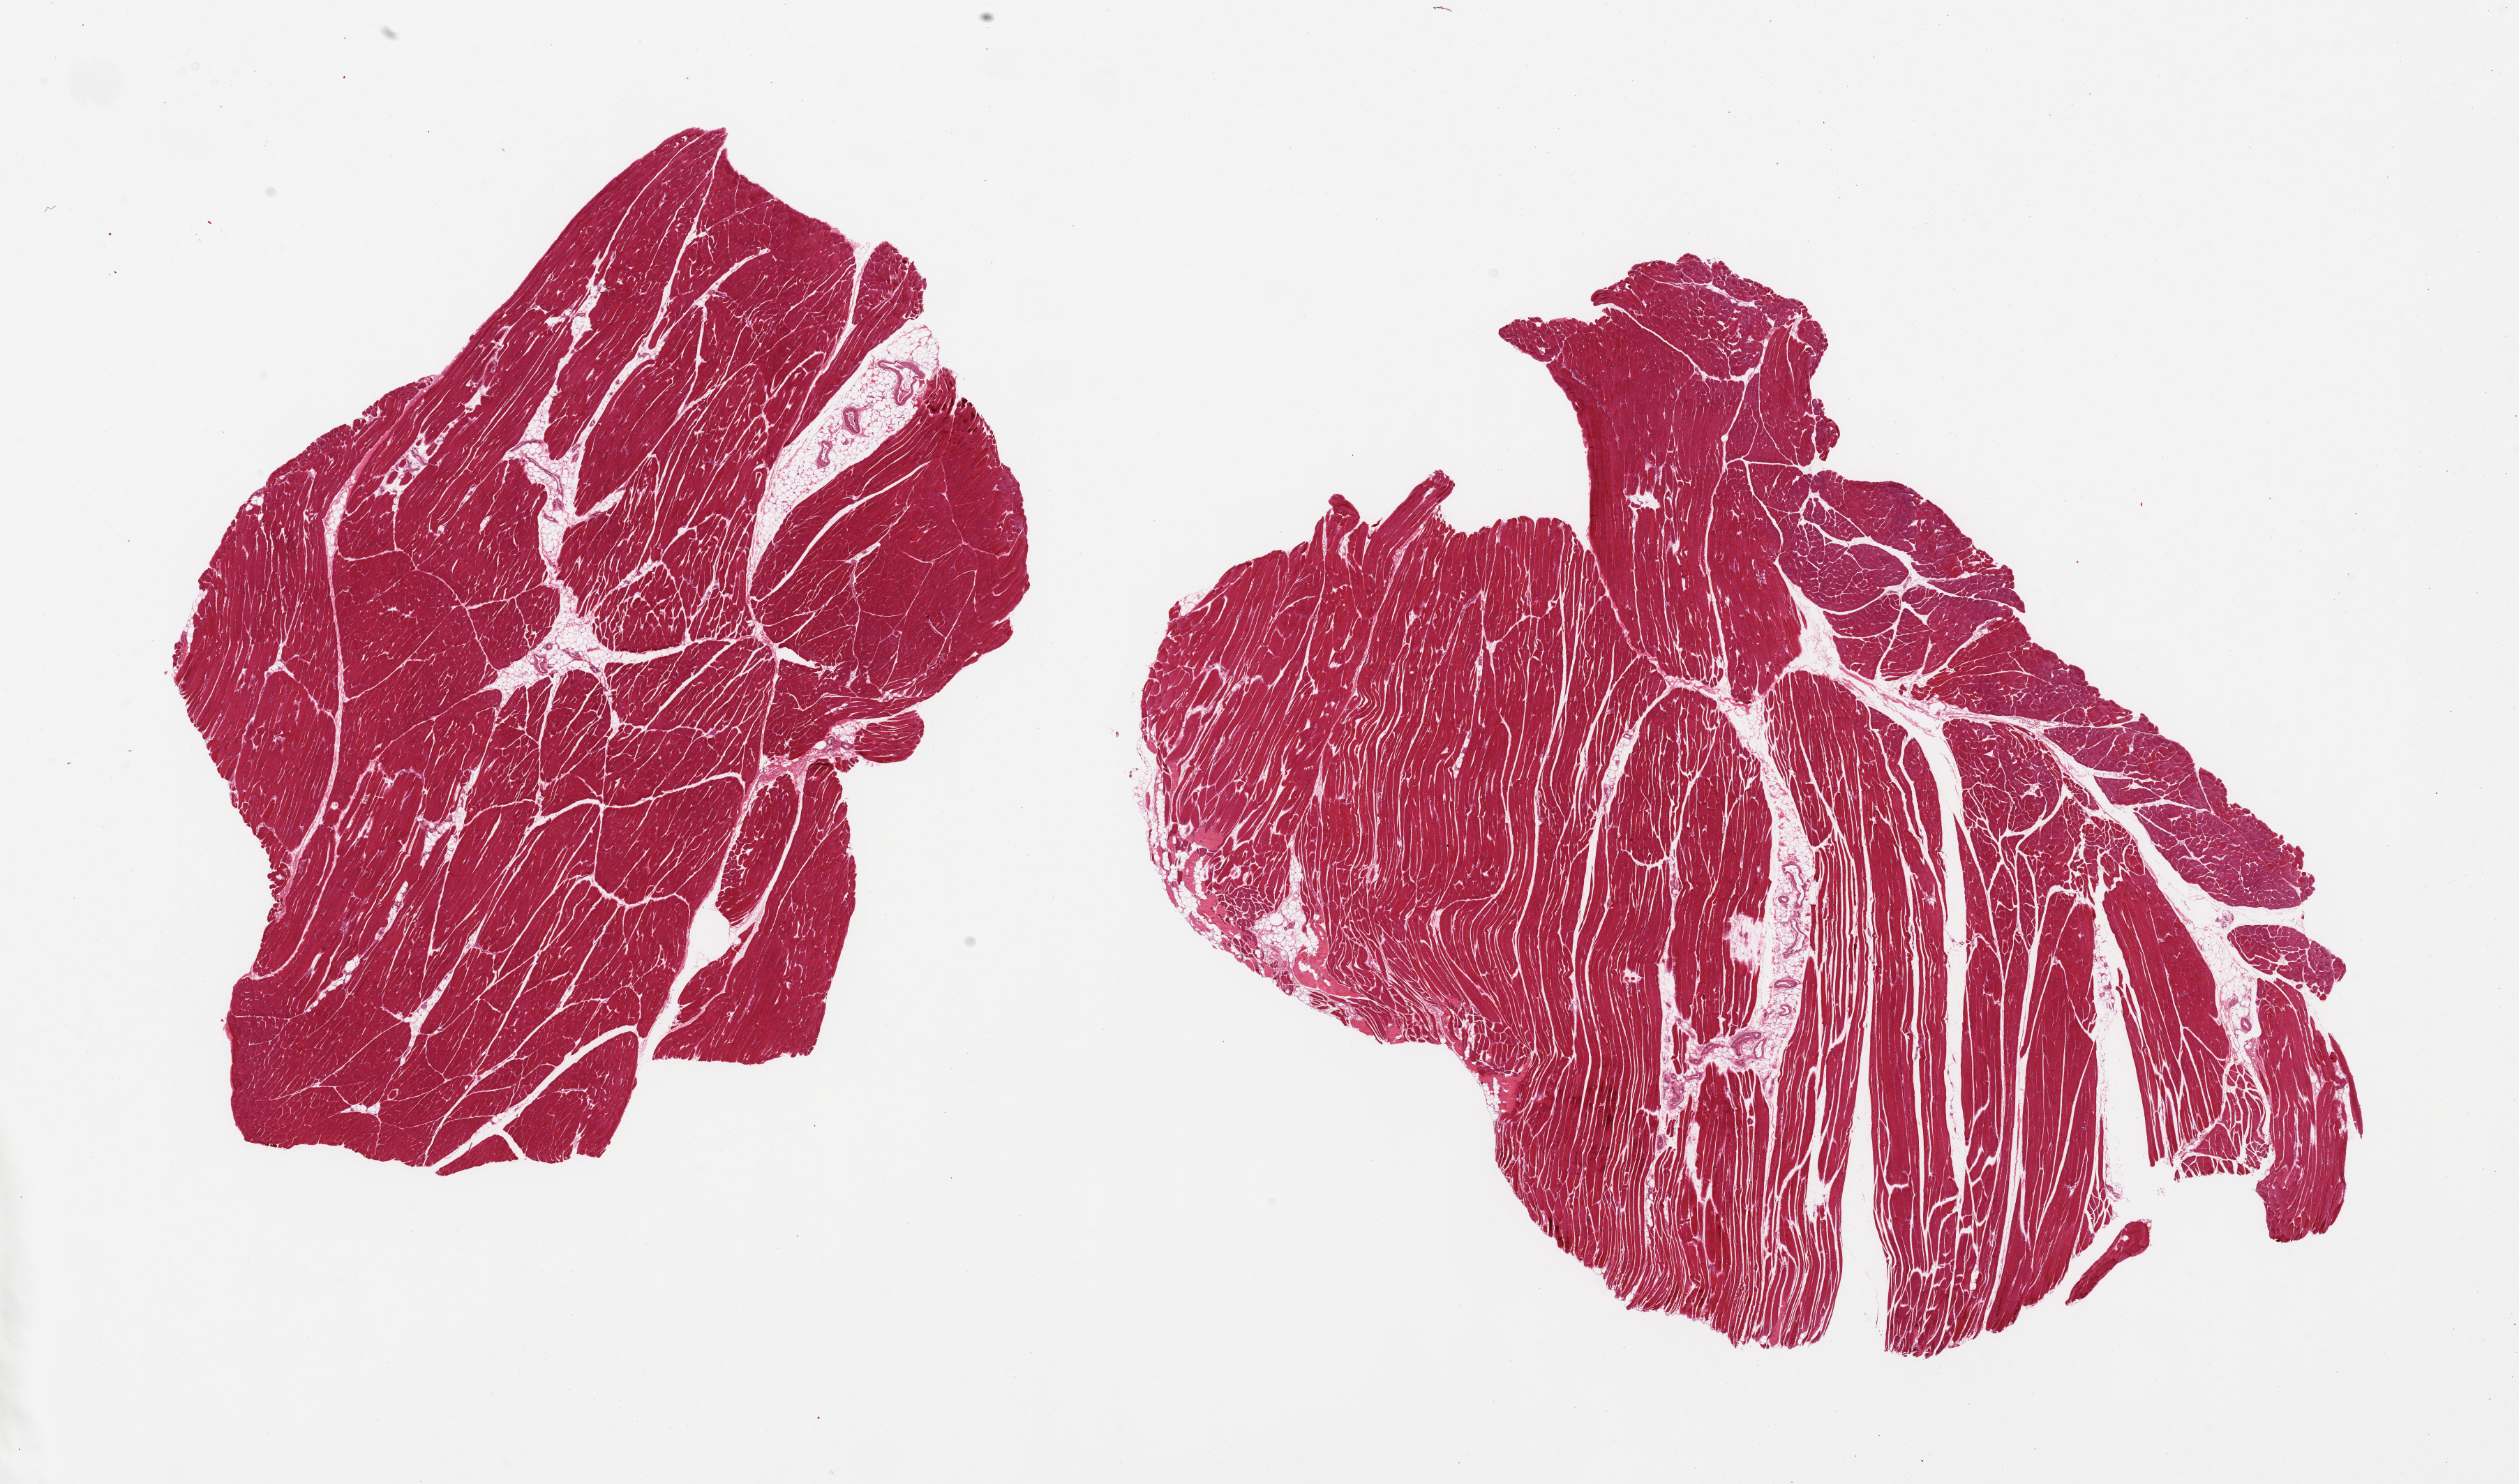
Digitized H&E-stained section — a low-resolution overview of the entire scanned area, about 28.5 x 16.8 mm. PAXgene-fixed, paraffin-embedded tissue. Section of skeletal muscle (target tissue). Tissue donor sample. Donor sex: male.
Review note (as recorded): 2 pieces, 10% internal fat, small portion of attached tendon.